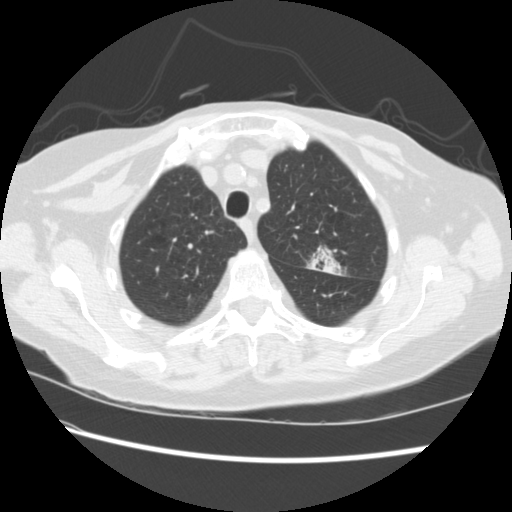
Low-dose screening chest CT, axial slice, first (baseline) screen, lung window (W 1500 / L -600 HU), 2.5 mm slice thickness. Female participant, aged 74 years at enrolment. Former smoker at enrolment.
• Expert reader's lesion annotation, bounding box (x1, y1, x2, y2) in pixels: (297, 240, 347, 281).
• The screening reader recorded 2 non-calcified nodules or masses ≥4 mm on this exam (left upper lobe, right lower lobe); which of them this box marks is not recorded.
• Official screen result: positive, change unspecified: nodule(s) >= 4 mm or enlarging nodule(s), mass(es), or other non-specific abnormalities suspicious for lung cancer.
• Later outcome: lung cancer diagnosed 309 days after this screen — non-small cell carcinoma, left upper lobe, stage IV (AJCC 6th edition).